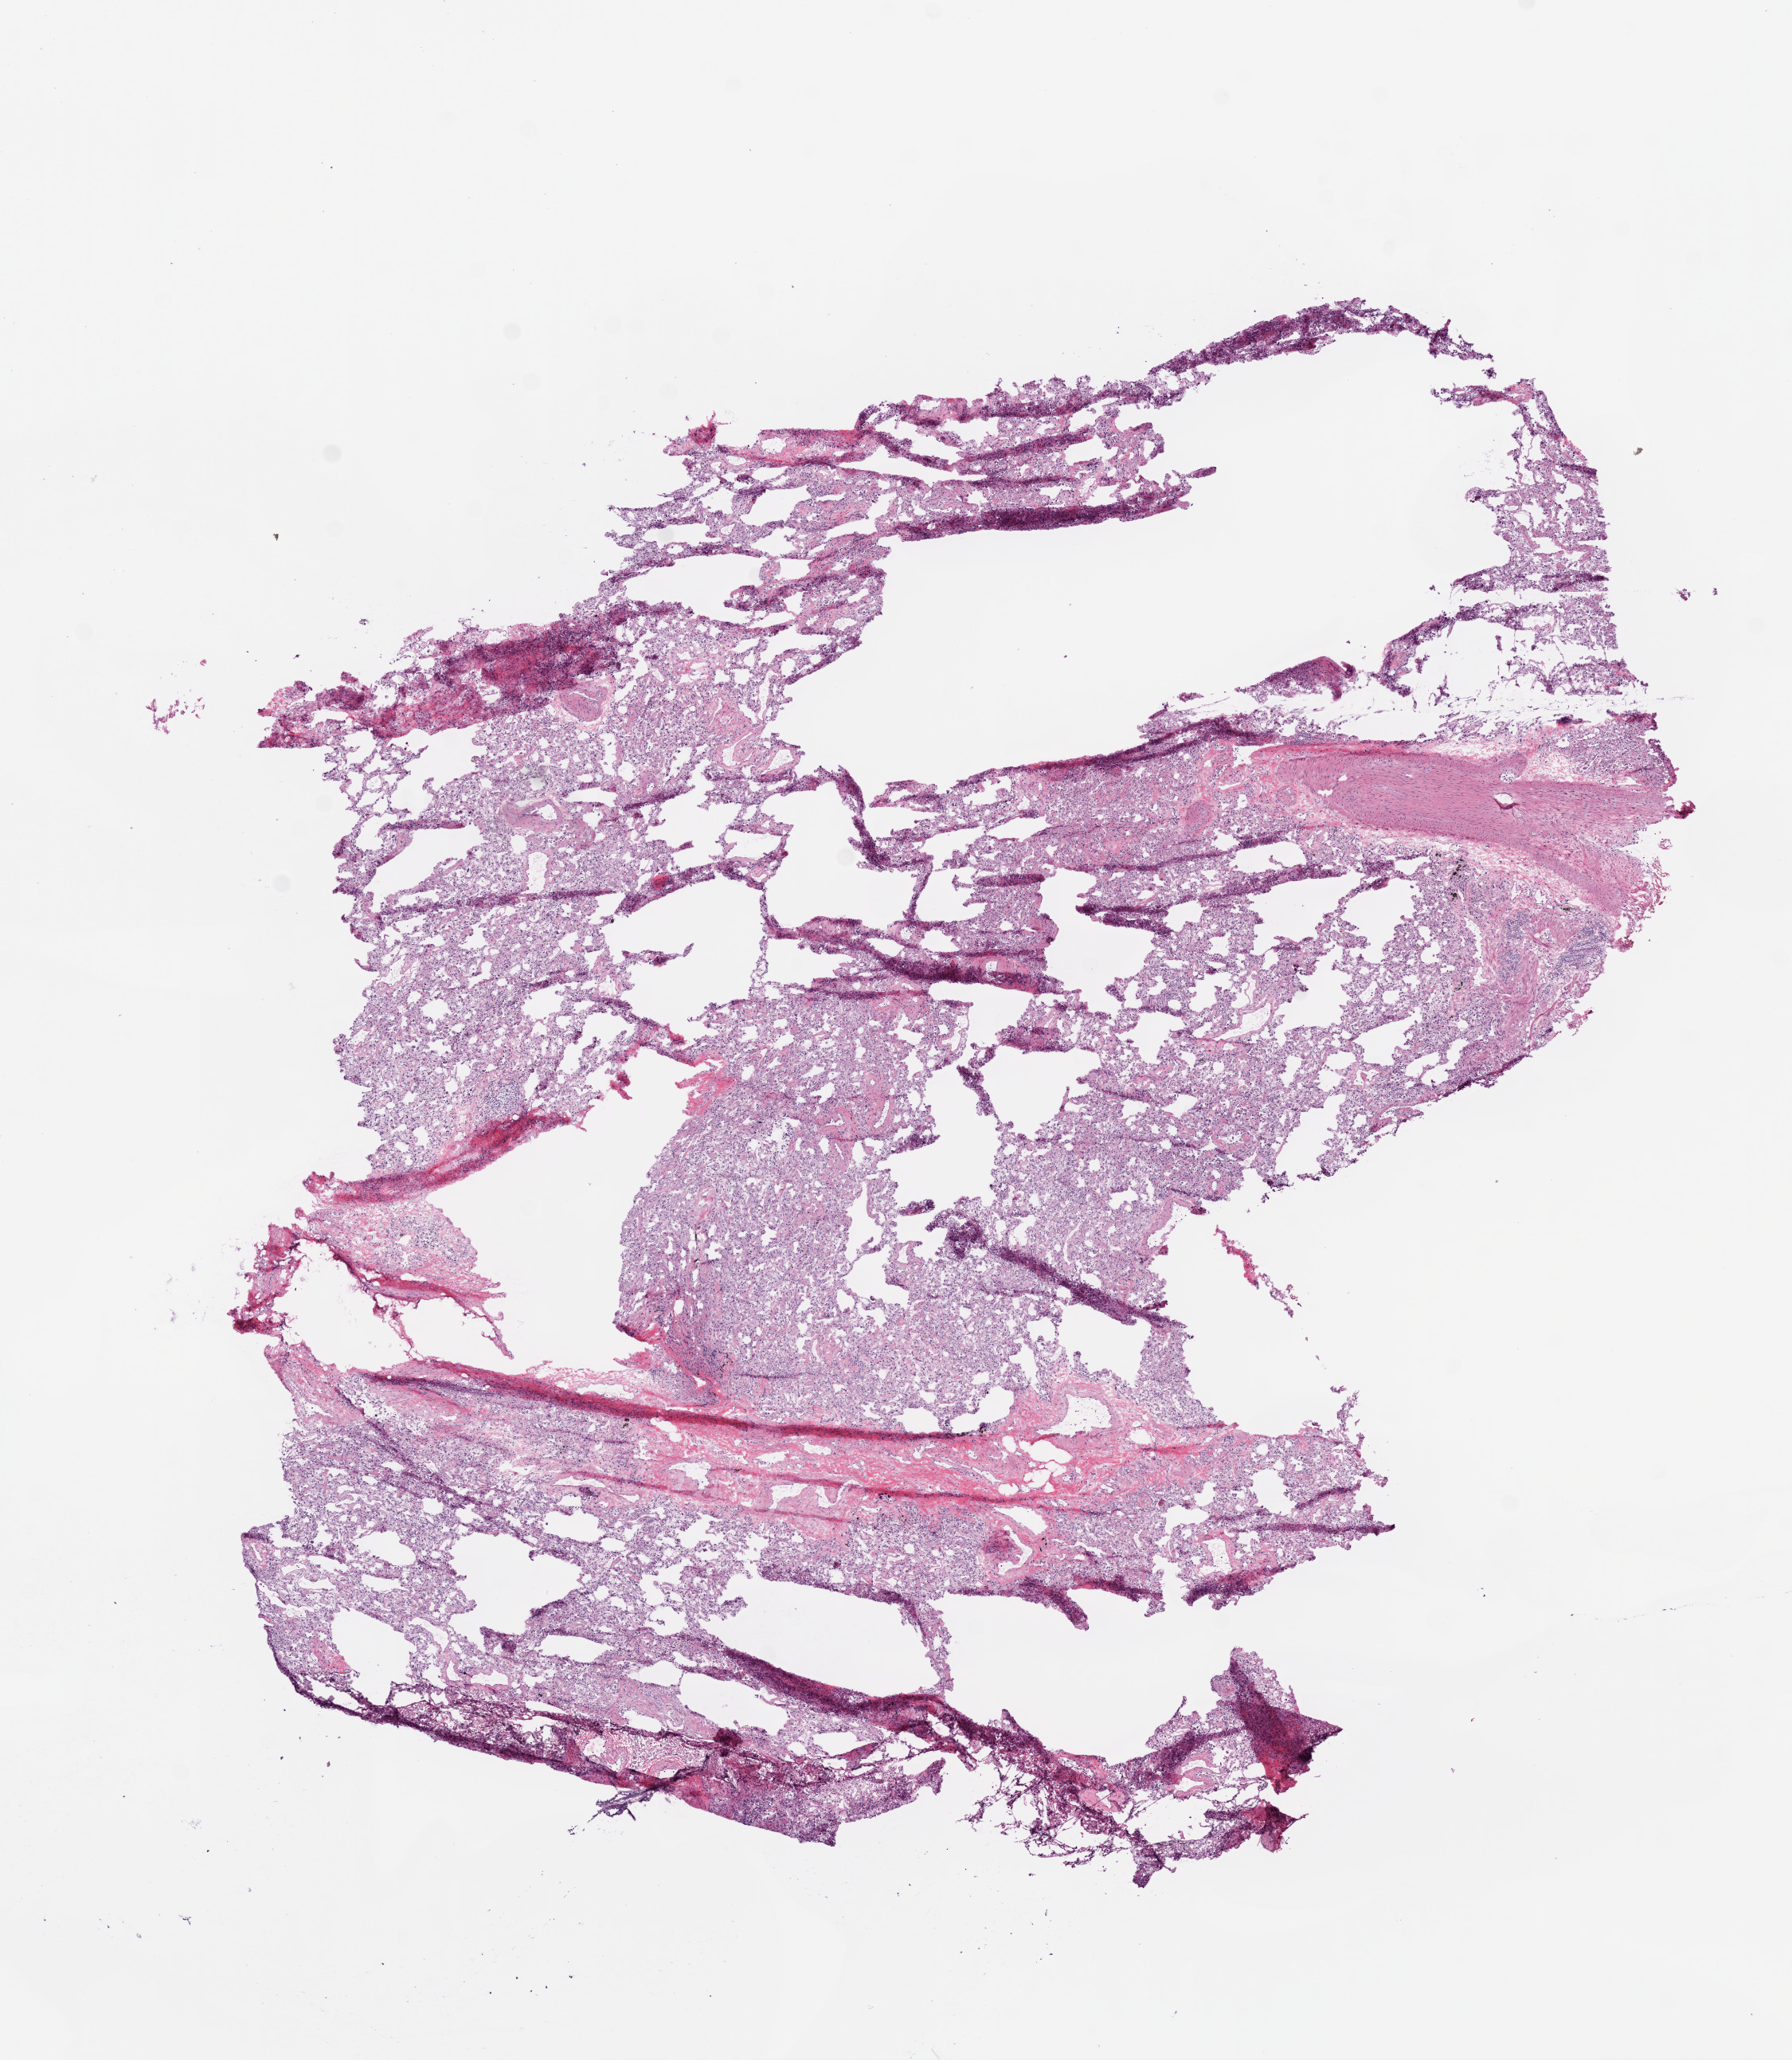
Whole-slide histology image, Hematoxylin and eosin (H&E) stained, a low-resolution overview of the entire scanned area, about 9.0 x 10.4 mm (from a 20x scan); frozen section; solid tissue normal (non-tumour tissue) sample from the lung. Male, age 66 years at initial diagnosis.
This section: solid tissue normal sample (biorepository sample class). Patient diagnosis: Squamous cell carcinoma, NOS.